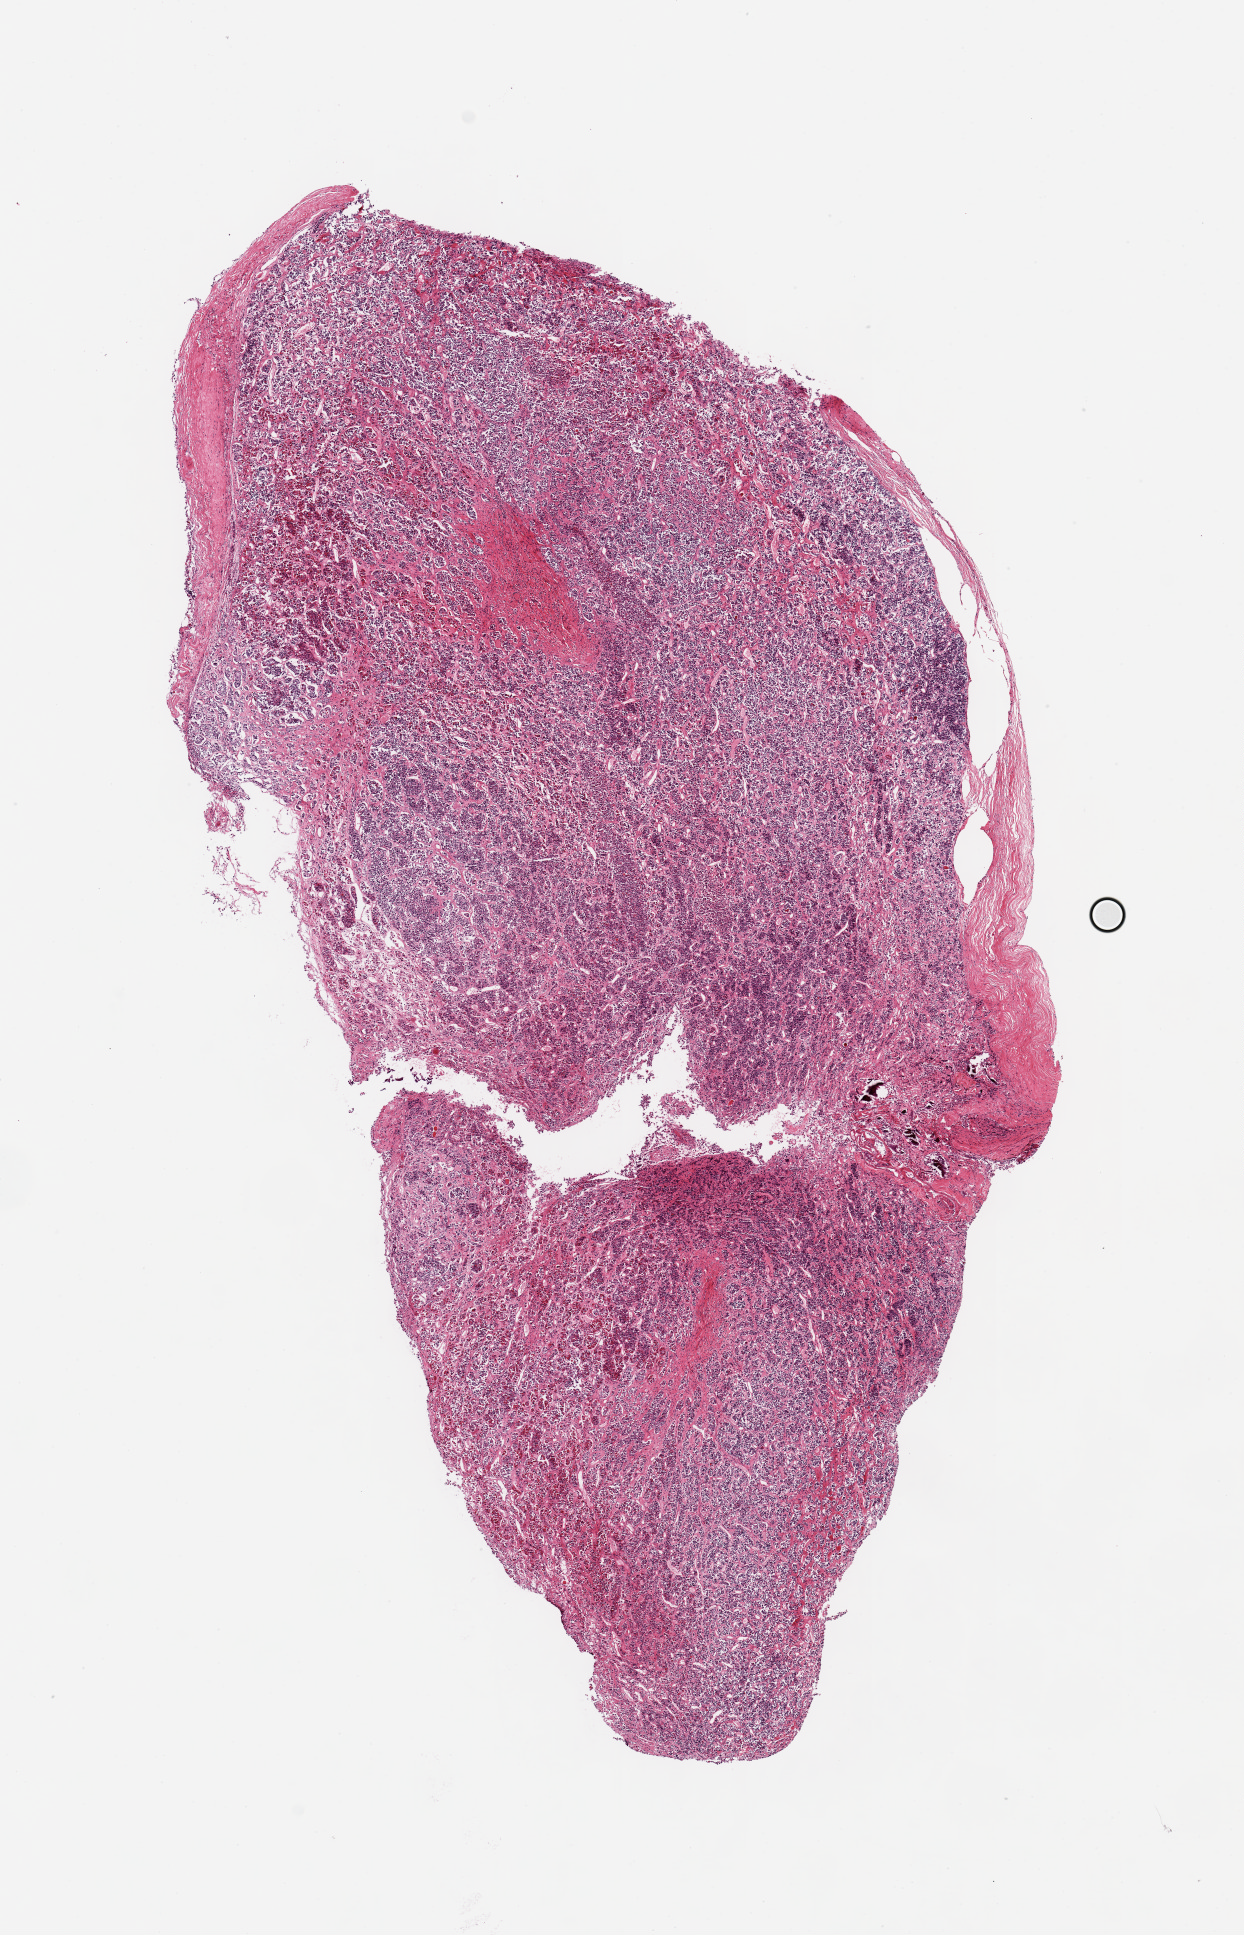
Digitized H&E-stained section — shown as a low-resolution overview of the whole scanned area (about 9.8 x 15.3 mm, from a 20x scan); PAXgene-fixed, paraffin-embedded tissue; section of pituitary (target tissue); tissue donor sample. Donor sex: female.
Pathologist's review note for this sample: 1 piece, 13x5.5mm; anterior; loss of cell cohesion.